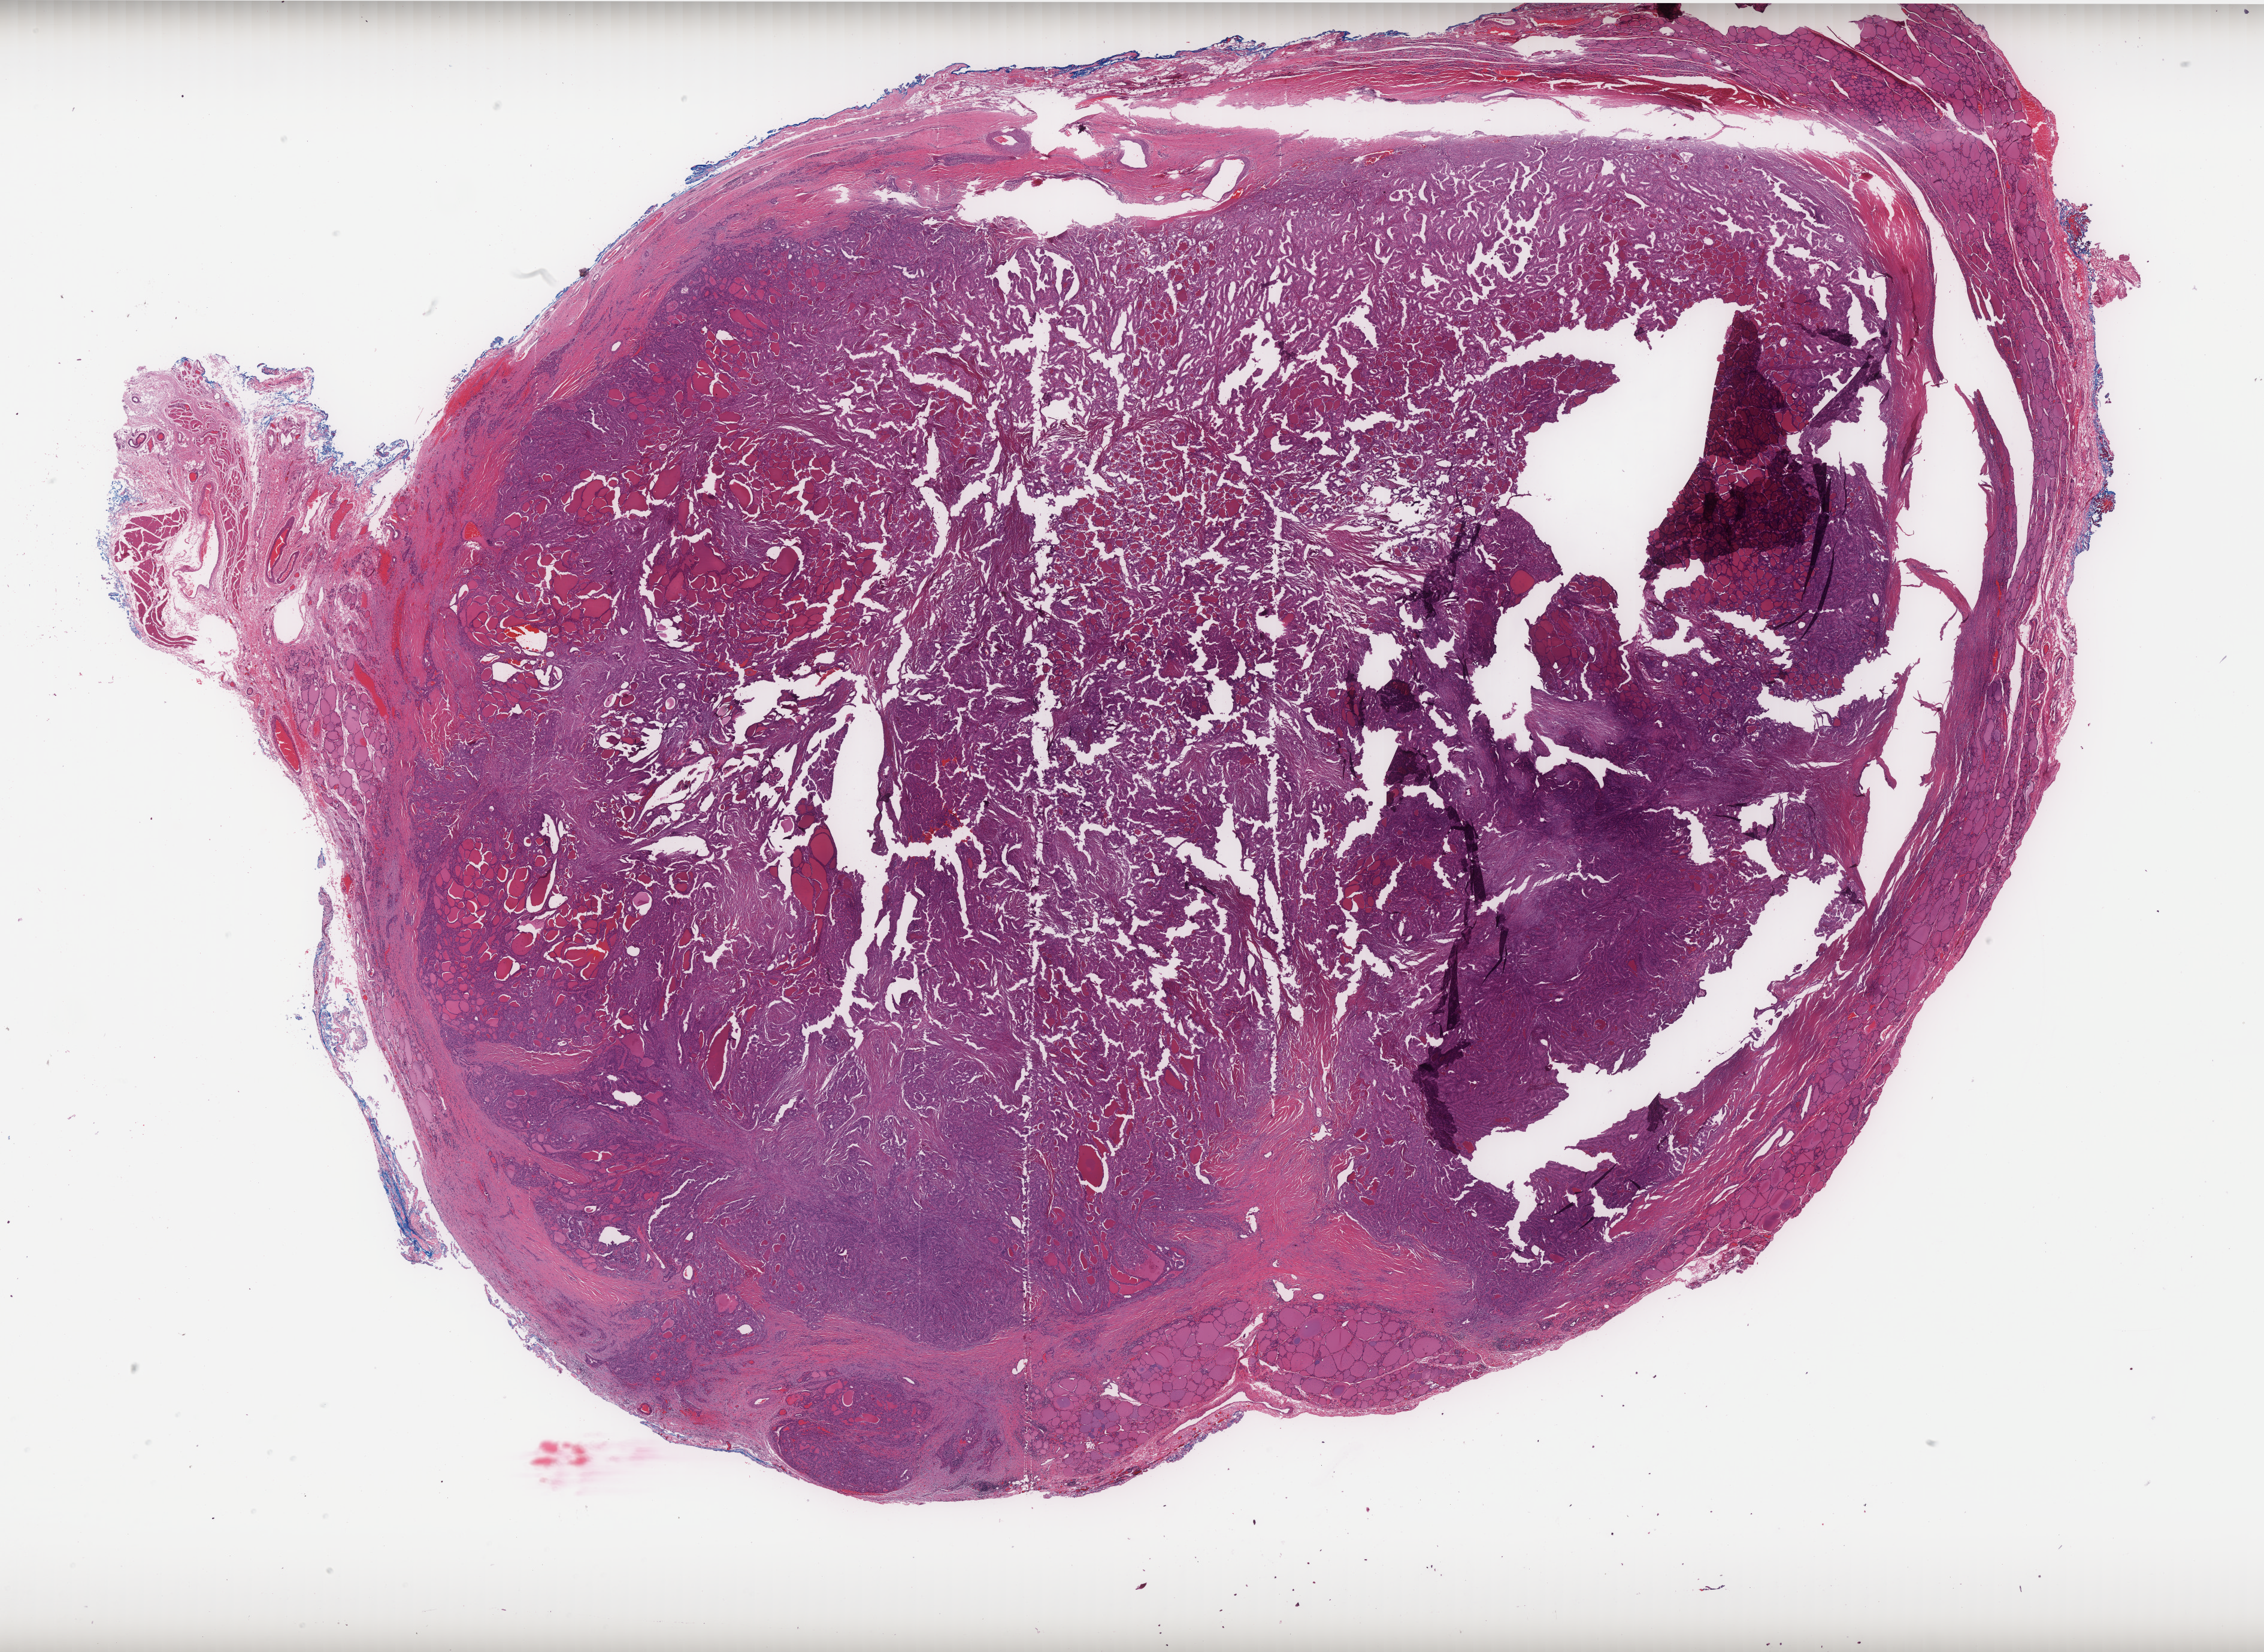
Whole-slide histology image, H&E — a low-resolution overview of the entire scanned area, about 30.3 x 22.1 mm (from a 40x scan); formalin-fixed paraffin-embedded (FFPE) diagnostic section; sample: primary tumour, thyroid. Male, age 58 years at initial diagnosis.
* lymph nodes positive (case pathology): 3 of 37 examined
* AJCC pathologic stage: IVA
* histologic diagnosis: Papillary adenocarcinoma, NOS (thyroid gland)